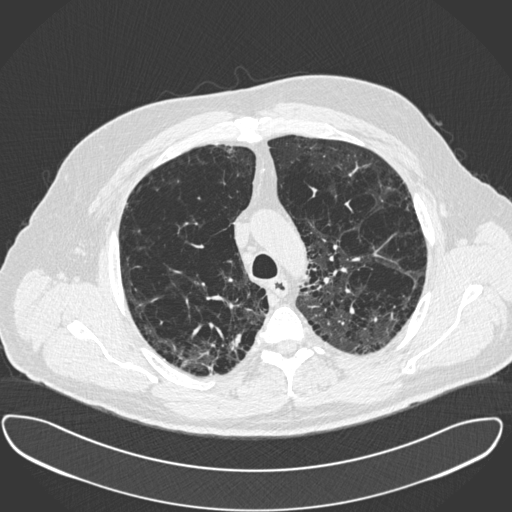
Low-dose screening chest CT, one axial slice. Position 290 of 385 along the scan axis. Reconstruction kernel B30f. 120 kVp. Lung window (W 1500 / L -600 HU). 512 × 512 image matrix, field of view 408 × 408 mm.
Structures marked on this image (expert manual segmentation):
- lesion 1 (tumor, upper lobe of right lung): bounding box (x1, y1, x2, y2) in pixels: (231, 334, 242, 350)